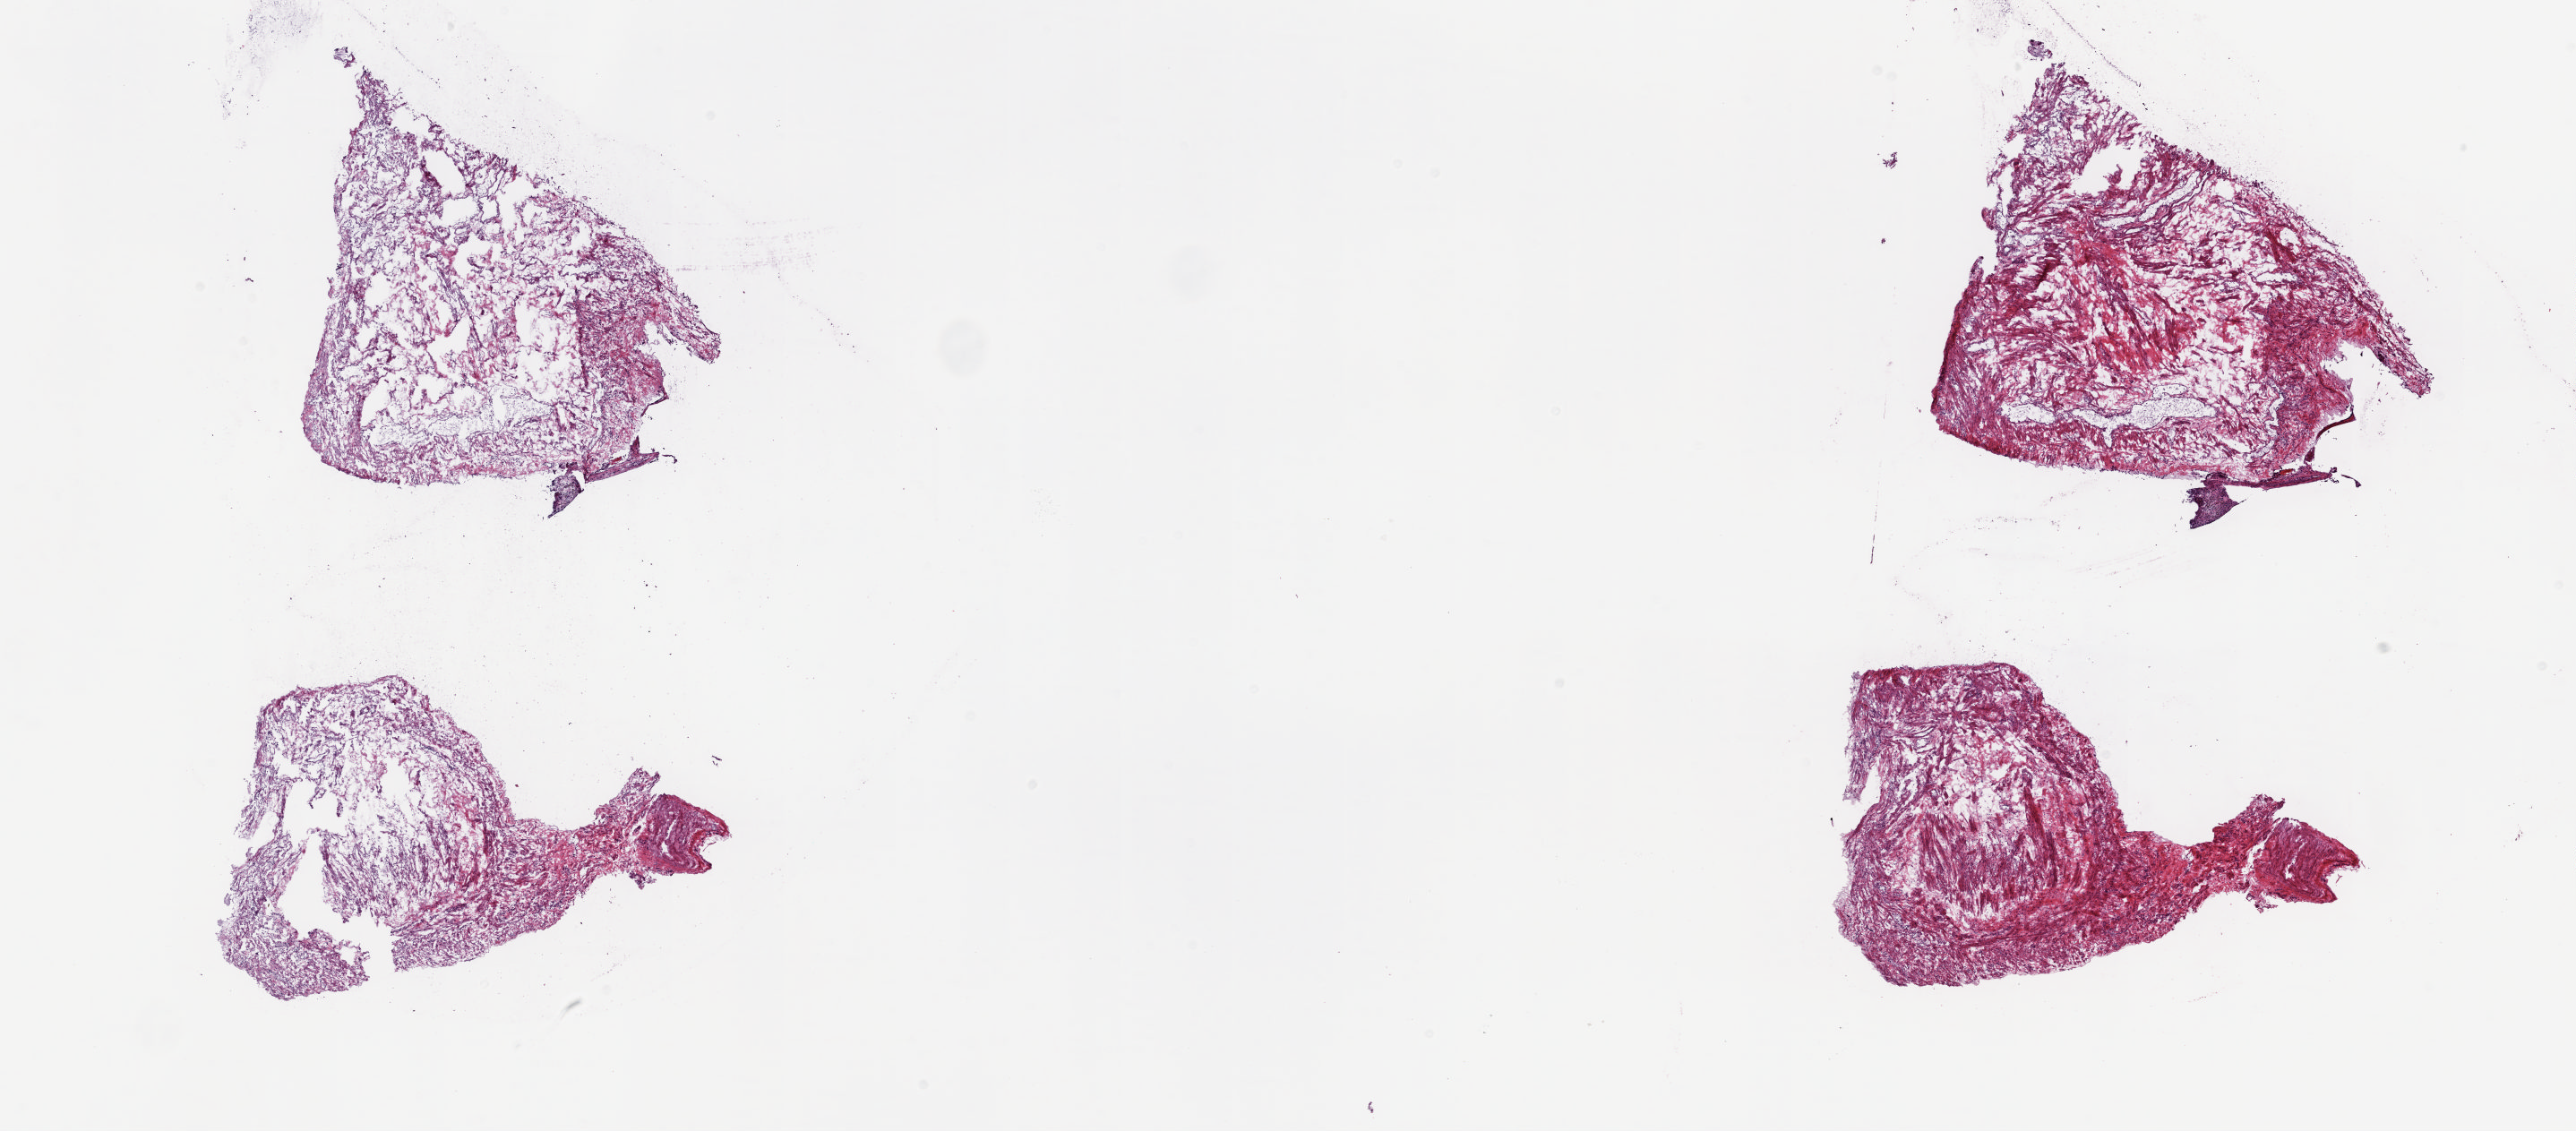
H&E-stained whole-slide image — low-resolution overview of the scanned area, about 22.8 x 10.0 mm, frozen section, sample: solid tissue normal (non-tumour tissue), uterus. Female patient; age at initial diagnosis 58 years. Composition of this section per pathologist review: tumour cells 0%, normal cells 100%.
- this section: solid tissue normal (non-tumour) sample from the same patient
- patient diagnosis: Endometrioid adenocarcinoma, NOS